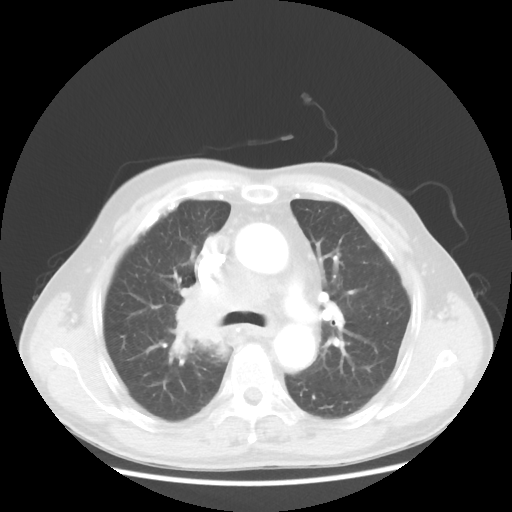
Chest CT, one axial slice. Slice 81 of 124 in the series (ordered by position). Reconstruction kernel STANDARD. 100 kVp. Lung window (W 1500 / L -600 HU). 5 mm slice thickness. 512 × 512 image matrix, field of view 382 × 382 mm. Patient: male, 64 years. From the clinical record (not read from this slice): clinical TNM (as recorded): T3 N3 M0; histopathological grade: G3.
Outlined on this slice (rectangle marked by the reading radiologist):
- lung tumour (recorded histology: small cell carcinoma): bounding box [x1, y1, x2, y2] px = [161, 278, 237, 370]